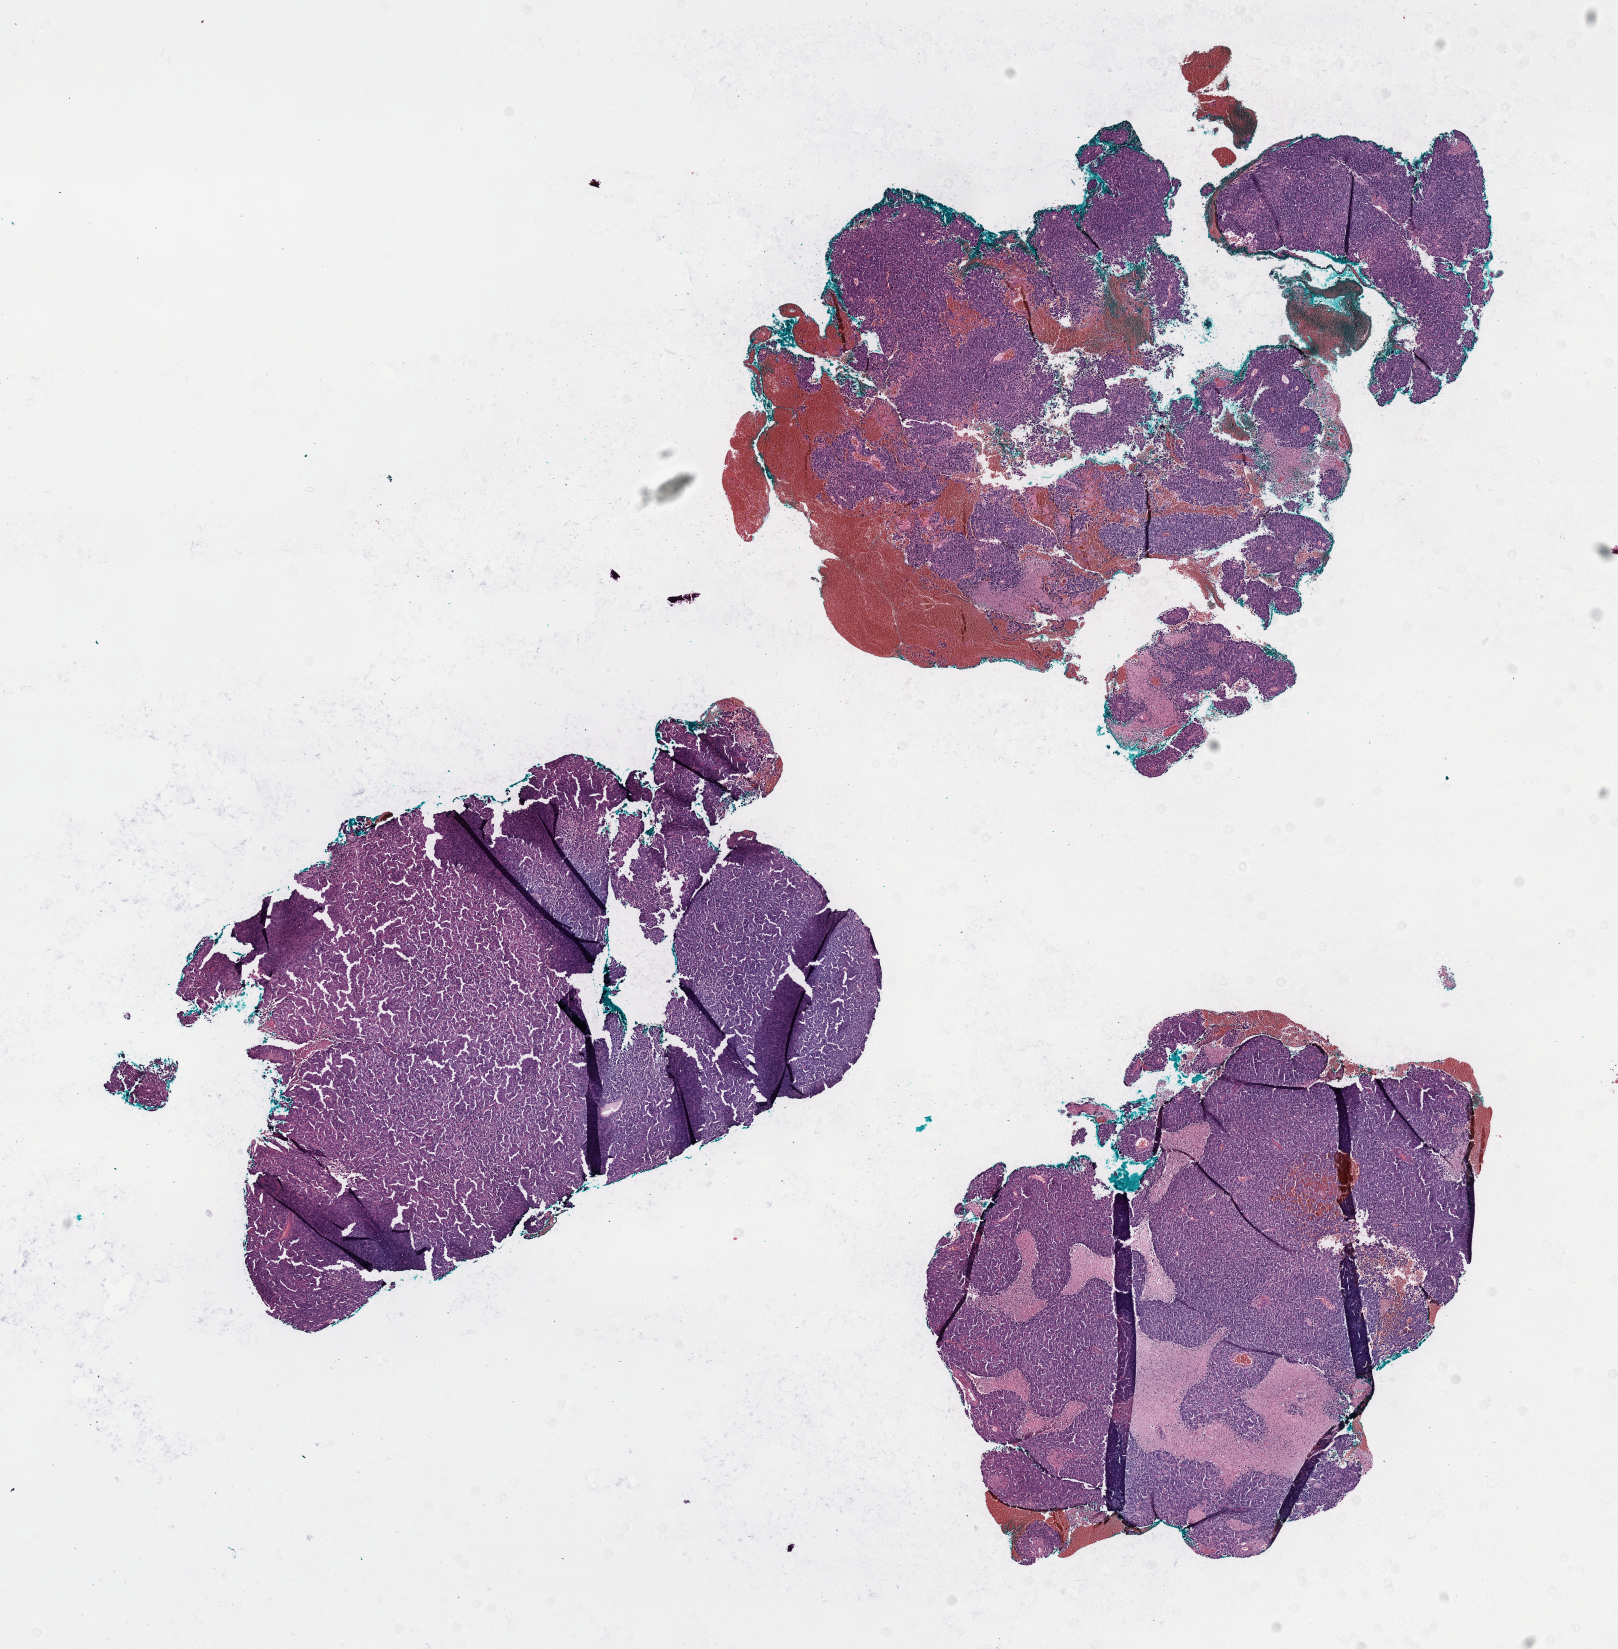
Digitized H&E-stained tissue section (whole slide) — low-resolution overview of the scanned area, about 13.1 x 13.3 mm, formalin-fixed paraffin-embedded (FFPE) diagnostic section, sample: primary tumour, cervix. Female patient; age at initial diagnosis 79 years. Histologic grade: G3 (poorly differentiated).
FIGO stage: IIIB. Diagnosis: Squamous cell carcinoma, NOS.